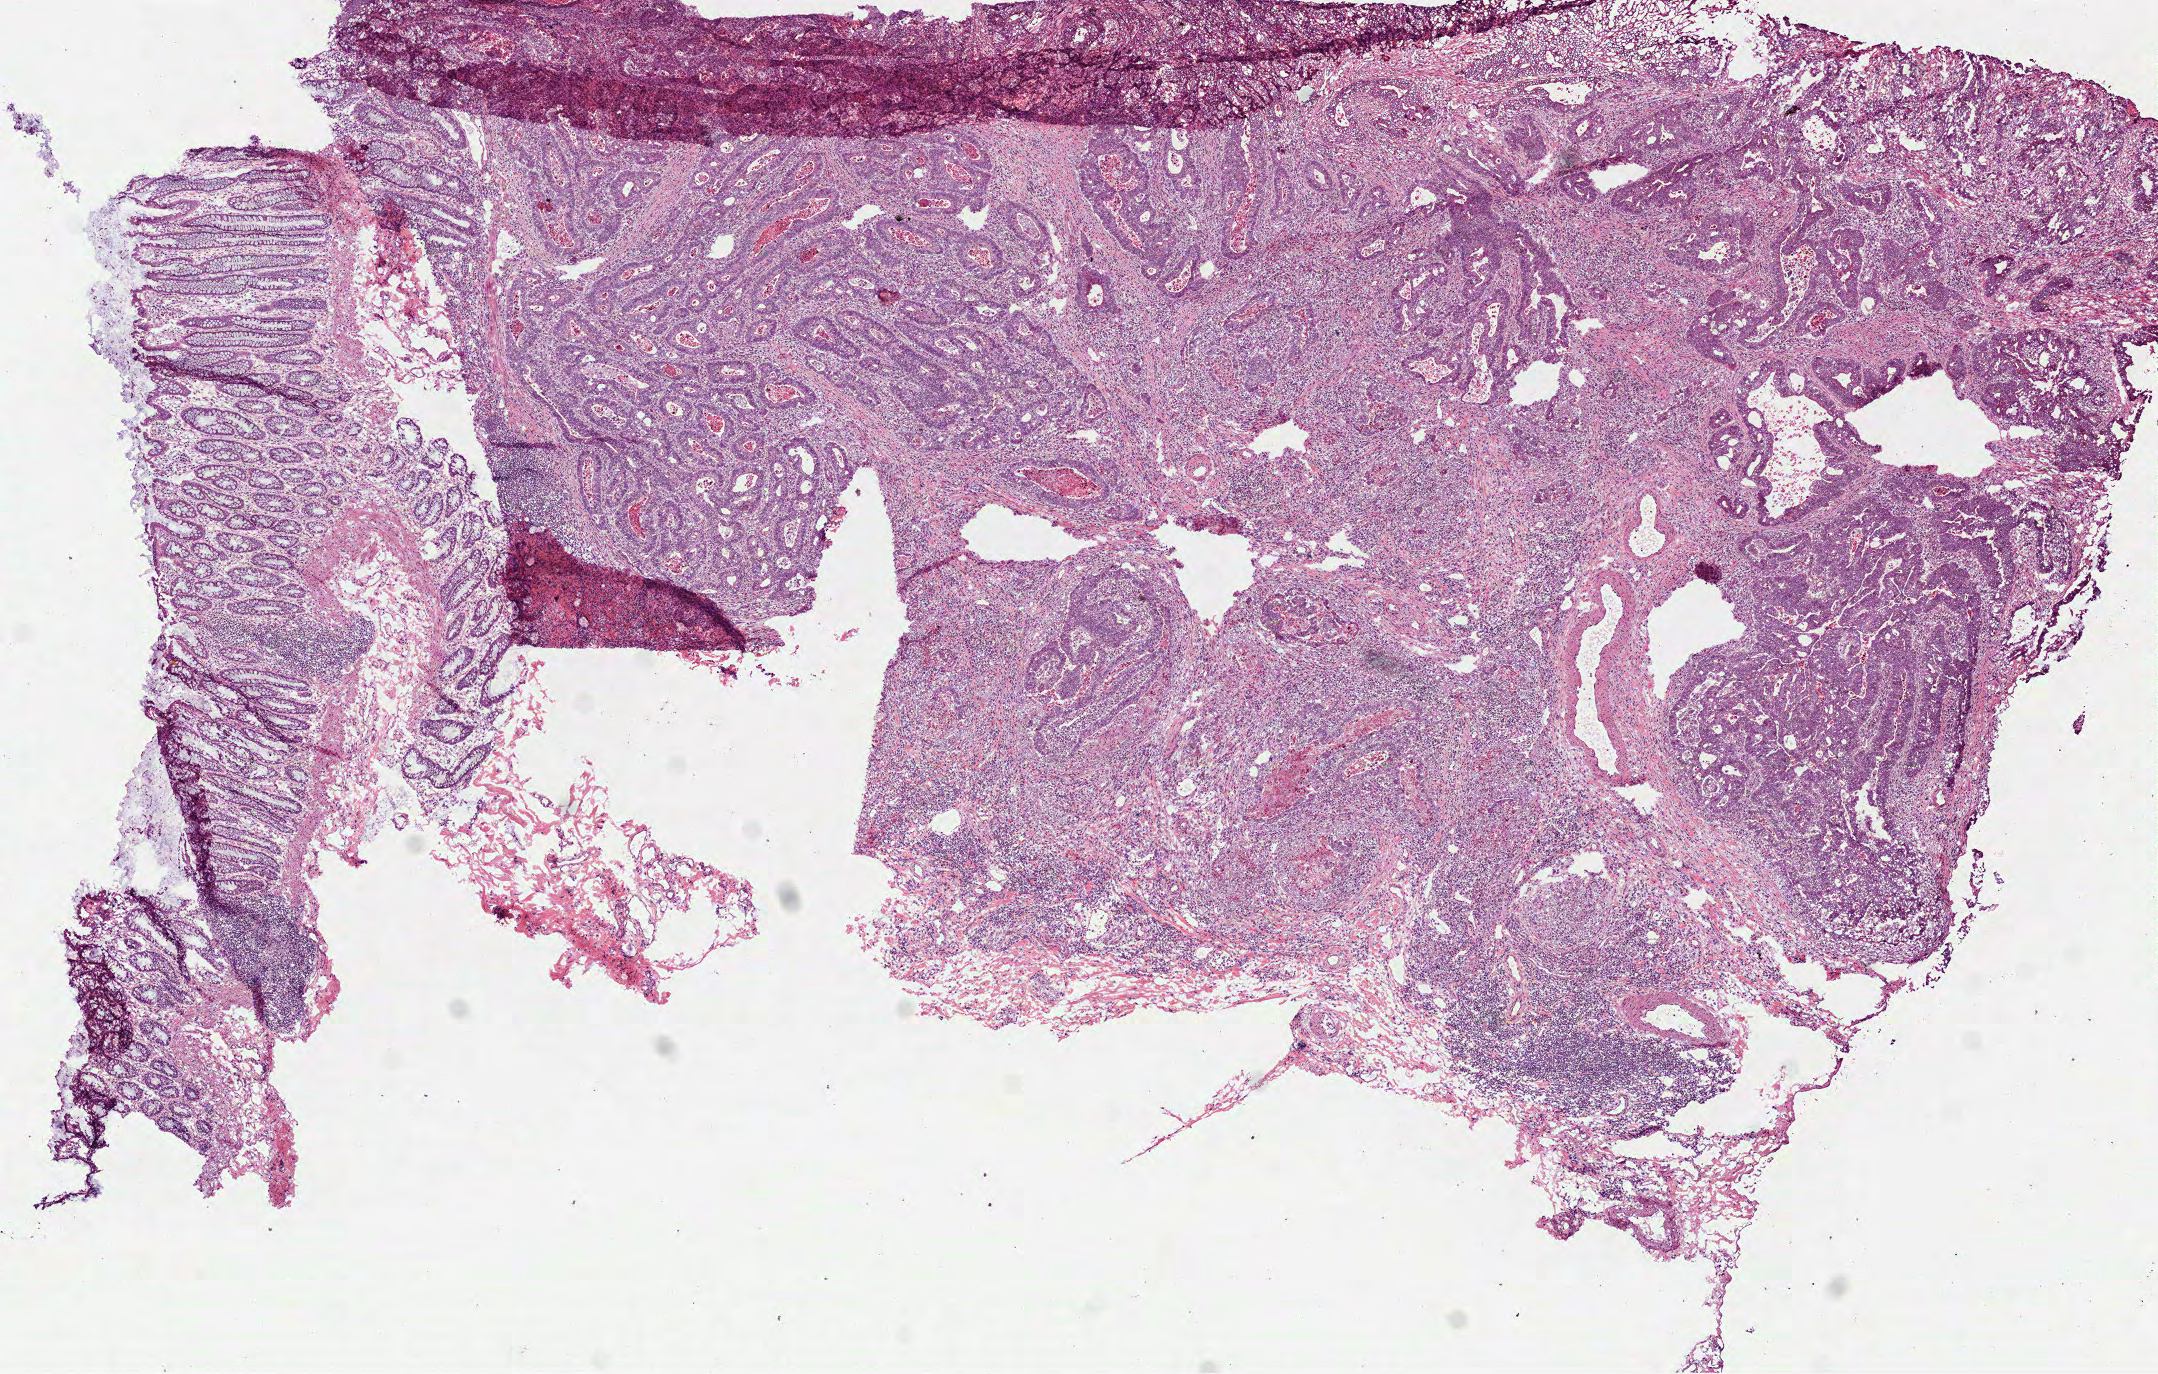
Hematoxylin and eosin (H&E) stained whole-slide image, whole scanned area (about 8.7 x 5.5 mm) shown as a low-resolution overview; frozen section; primary tumour sample from the colon. Female patient; age at initial diagnosis 77 years. Slide review estimates, as recorded: tumour cells 55%, tumour nuclei 60%, normal cells 10%, stromal cells 25%, necrosis 10%.
TNM: T3 N0 M0. AJCC pathologic stage: IIA (5th edition). Diagnosis: Adenocarcinoma, NOS (sigmoid colon).